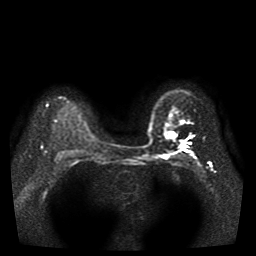
Breast MRI, one axial slice. Slice 32 of 41 in the series (ordered by position). Diffusion-weighted series; image 2 of 4 stored at this slice position (different b-values; order by instance number). 1.5 T. 5 mm slice thickness. 256 × 256 image matrix. Female patient.
Annotated regions visible in this slice (outlined manually by an expert reader):
- tumour on diffusion-weighted imaging: bounding box <179,142,187,148> (left, top, right, bottom; pixels)